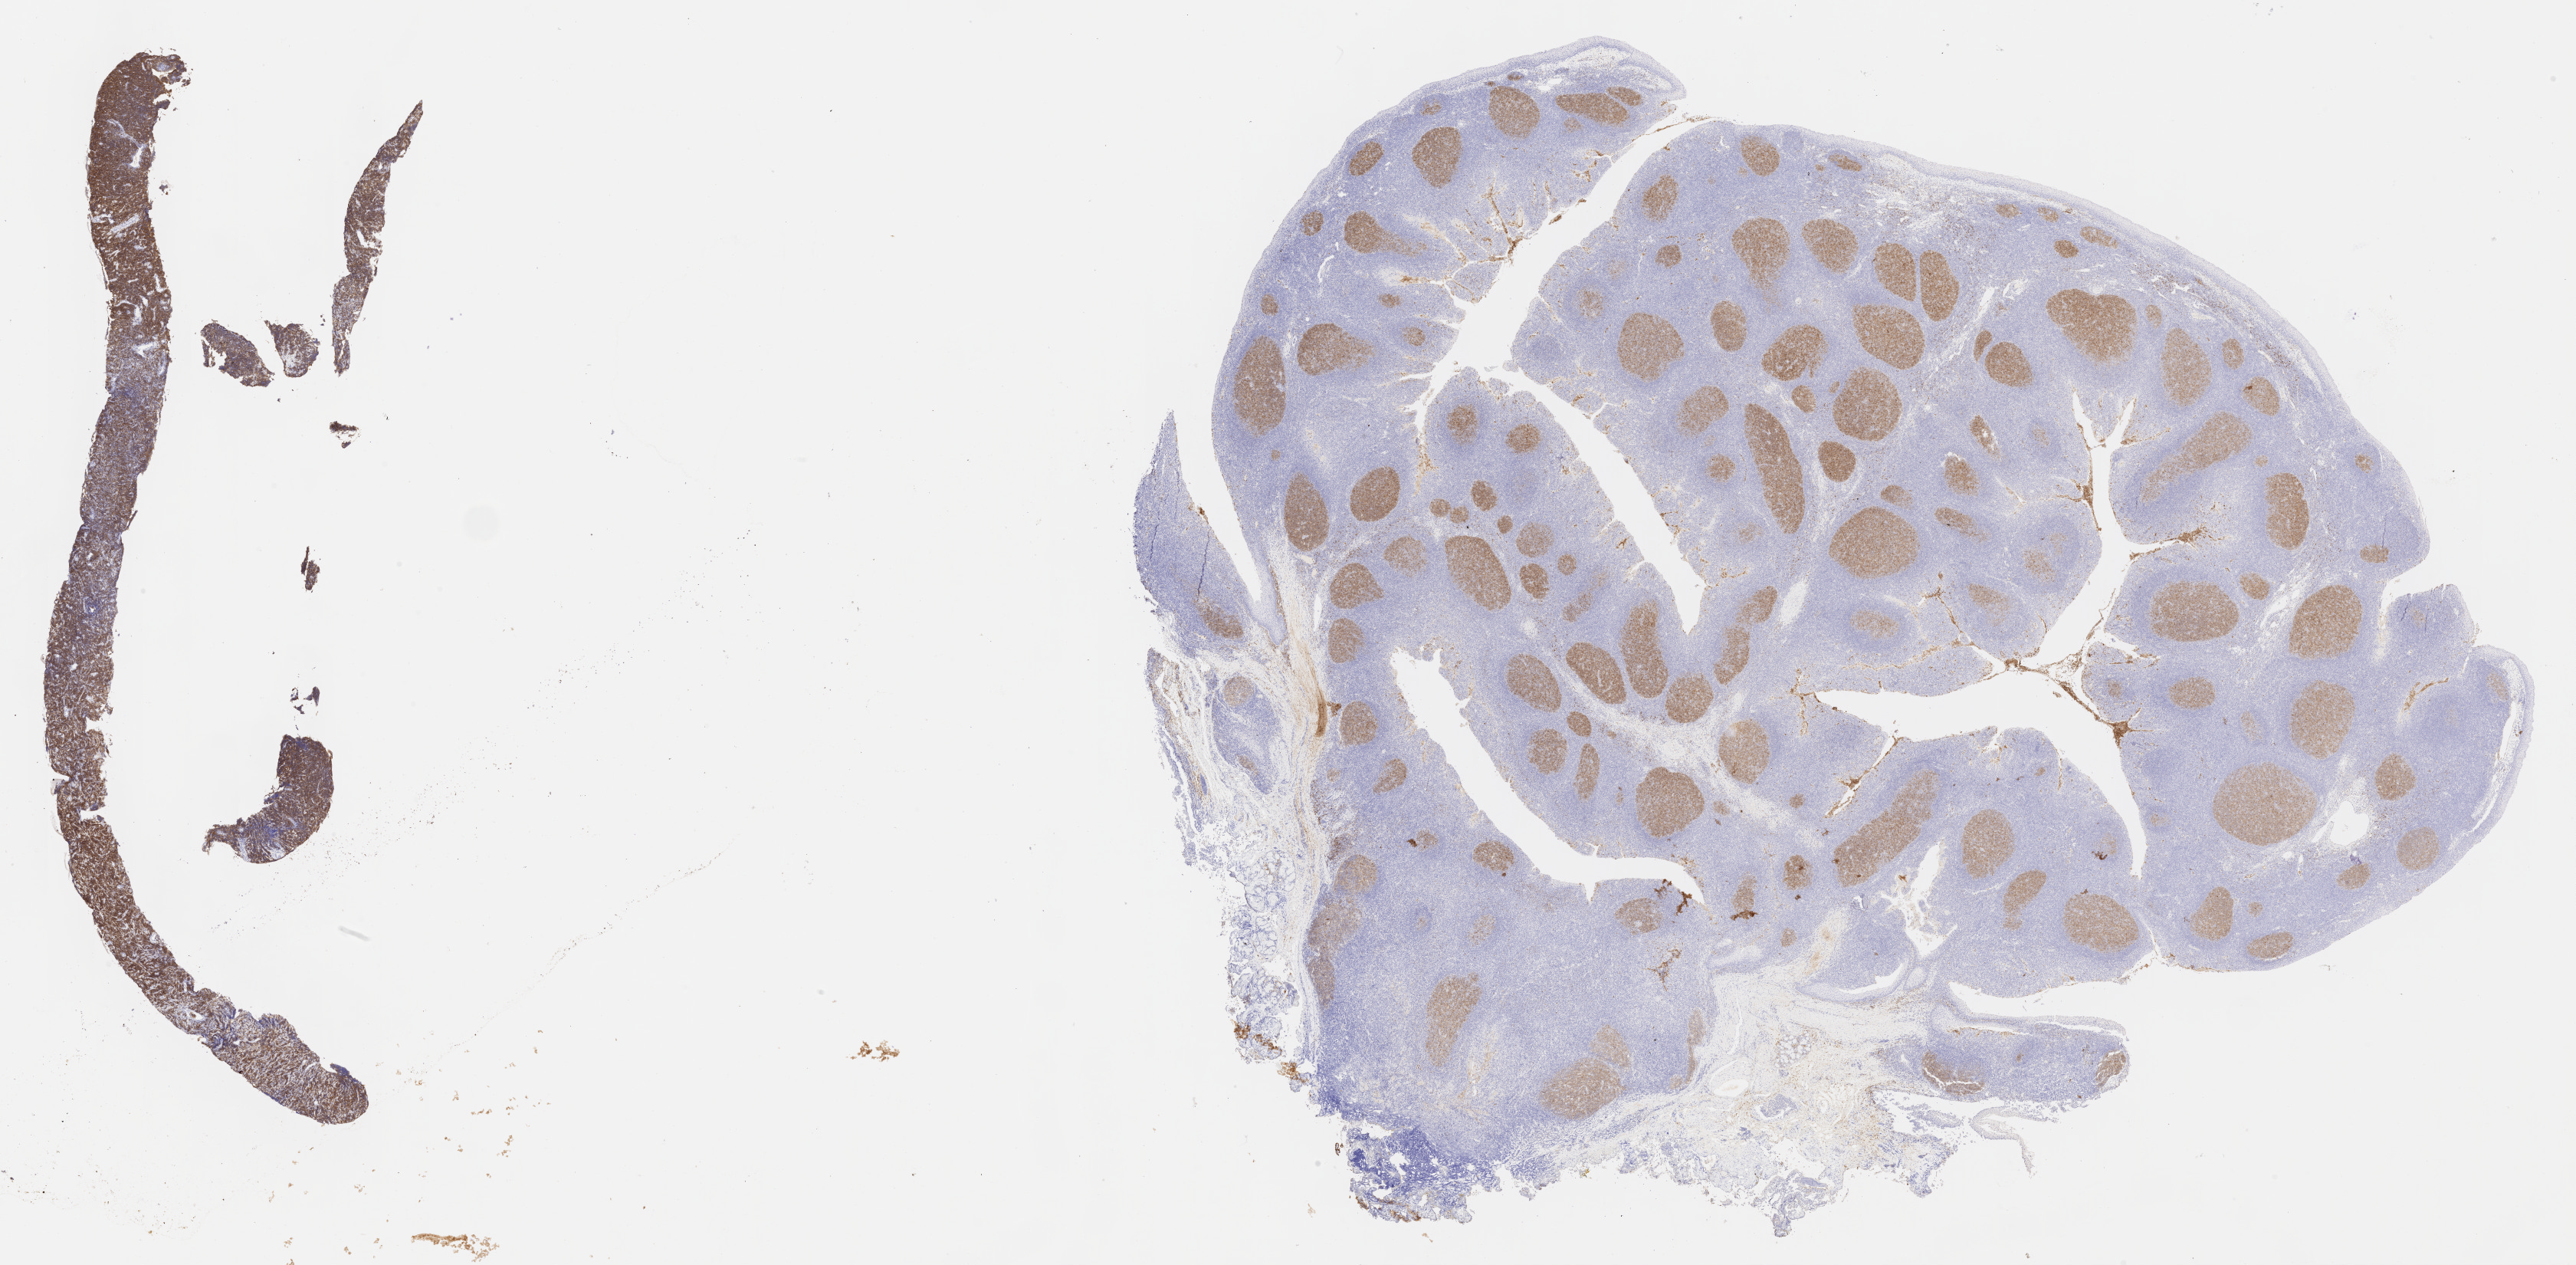
Whole-slide image, immunohistochemical stain for CD10 — whole scanned area (about 27.2 x 13.3 mm) shown as a low-resolution overview; tumor tissue; anatomic site: ovary. Patient: female, age at initial diagnosis 9 years.
- diagnosis: Burkitt lymphoma, NOS